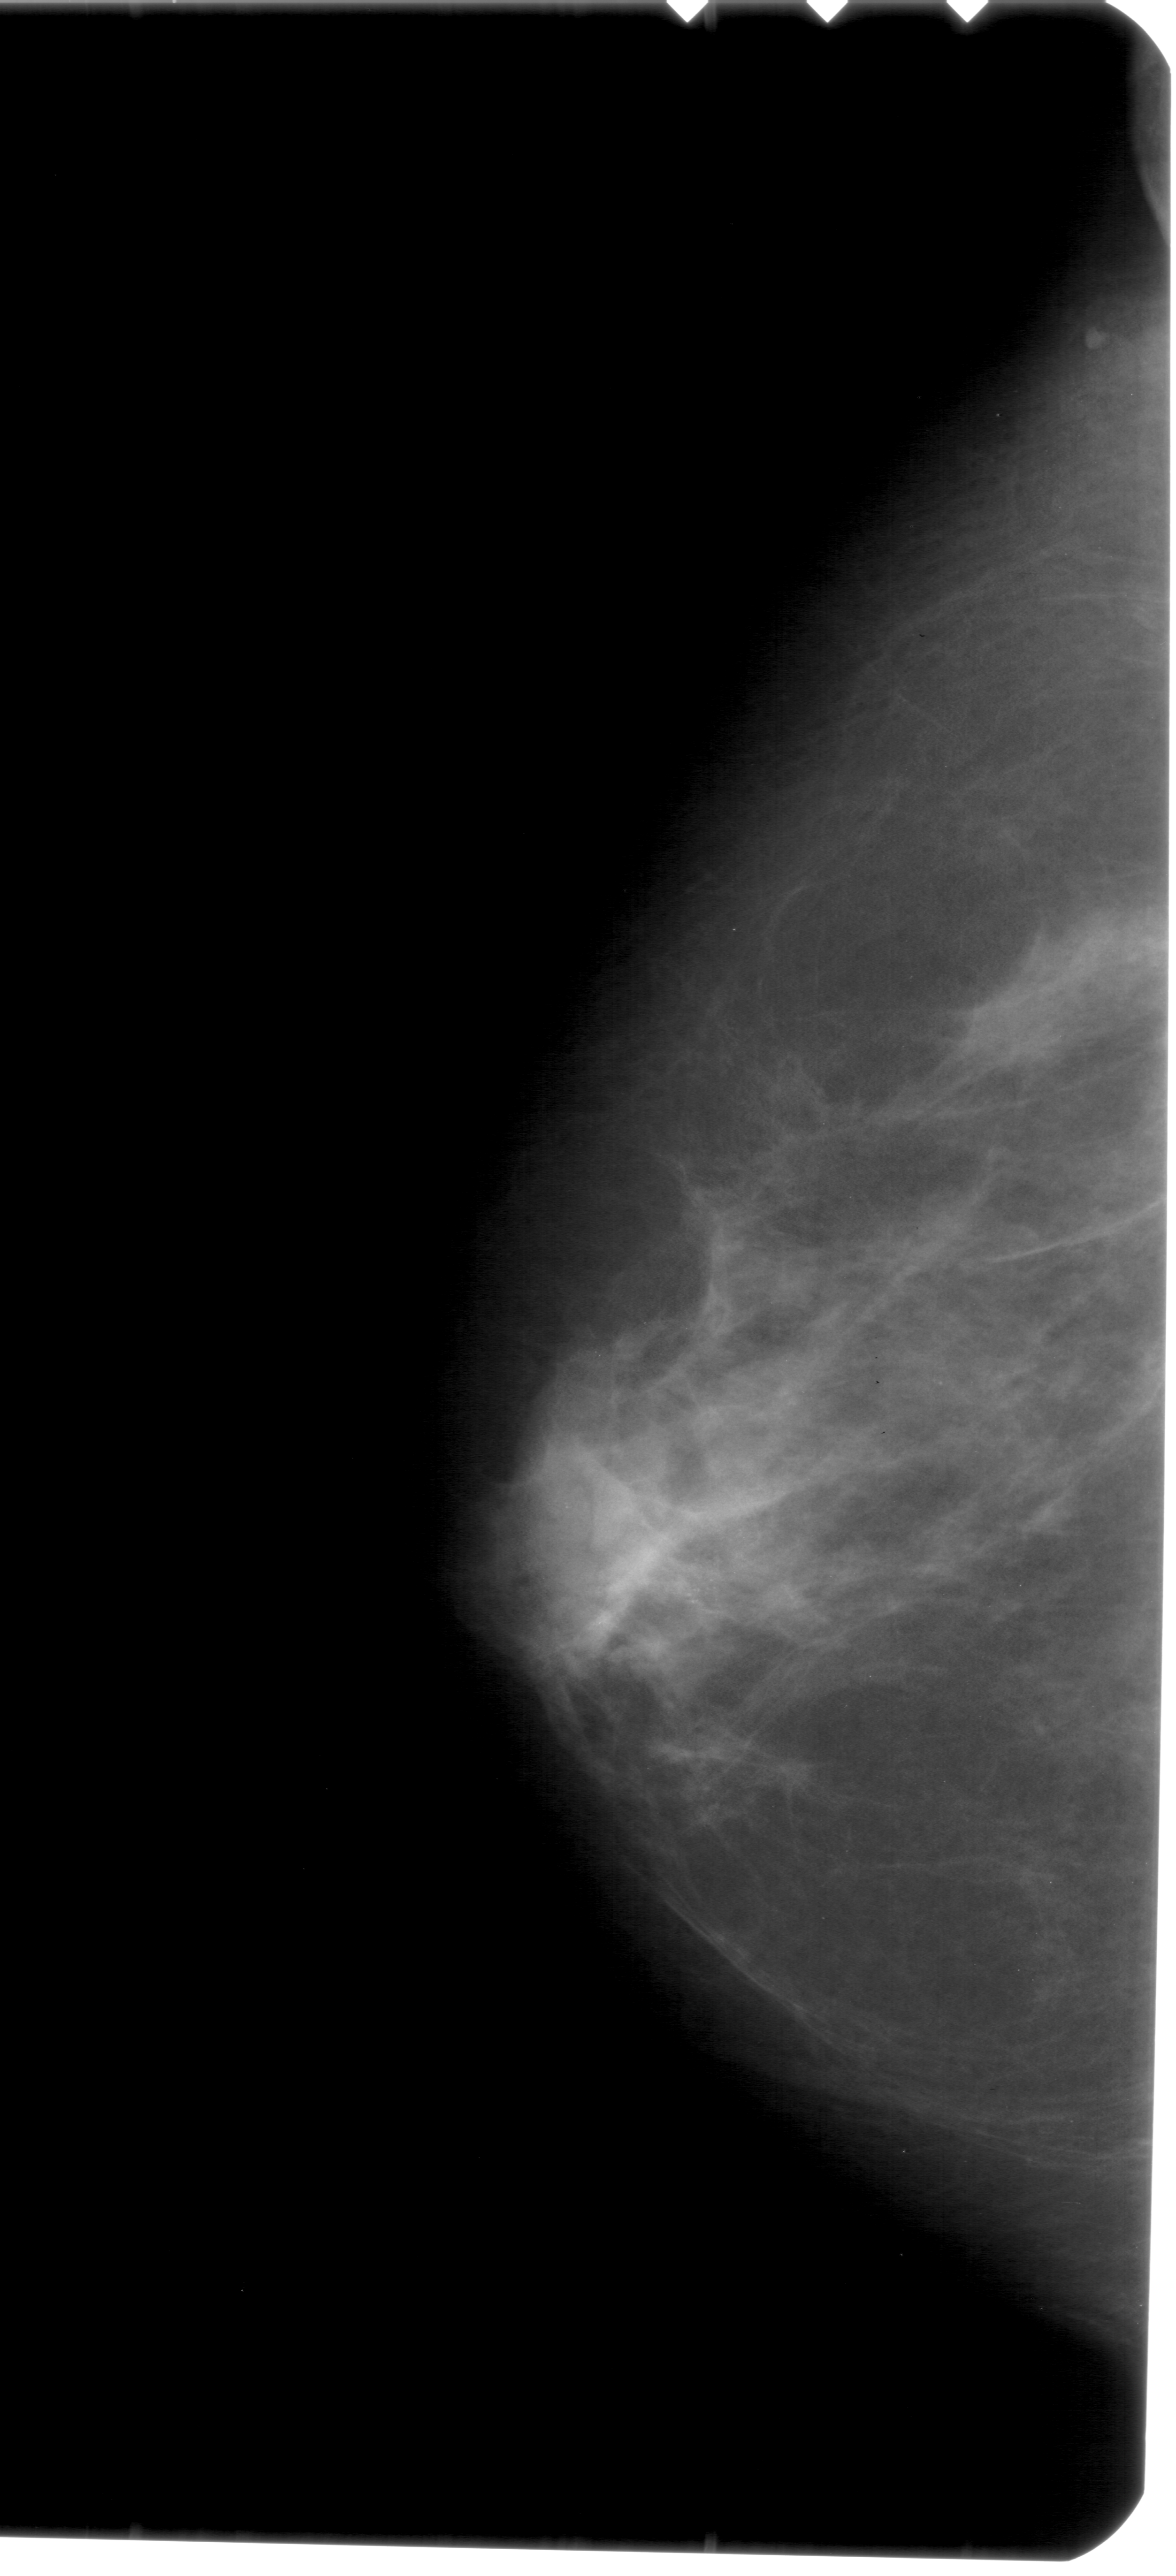
Digitized screen-film mammogram. Left breast. Craniocaudal (CC) view. Breast composition: scattered fibroglandular densities (BI-RADS density category 2 of 4). 1176 × 2576 image matrix.
Expert-marked regions of interest on this image (one box per marked abnormality):
- calcifications, morphology pleomorphic, distribution clustered; BI-RADS assessment category 4; subtlety rating 2 on a 1 (subtle) to 5 (obvious) scale; pathology (as recorded): benign: bounding box [x1, y1, x2, y2] px = [656, 1548, 823, 1639]